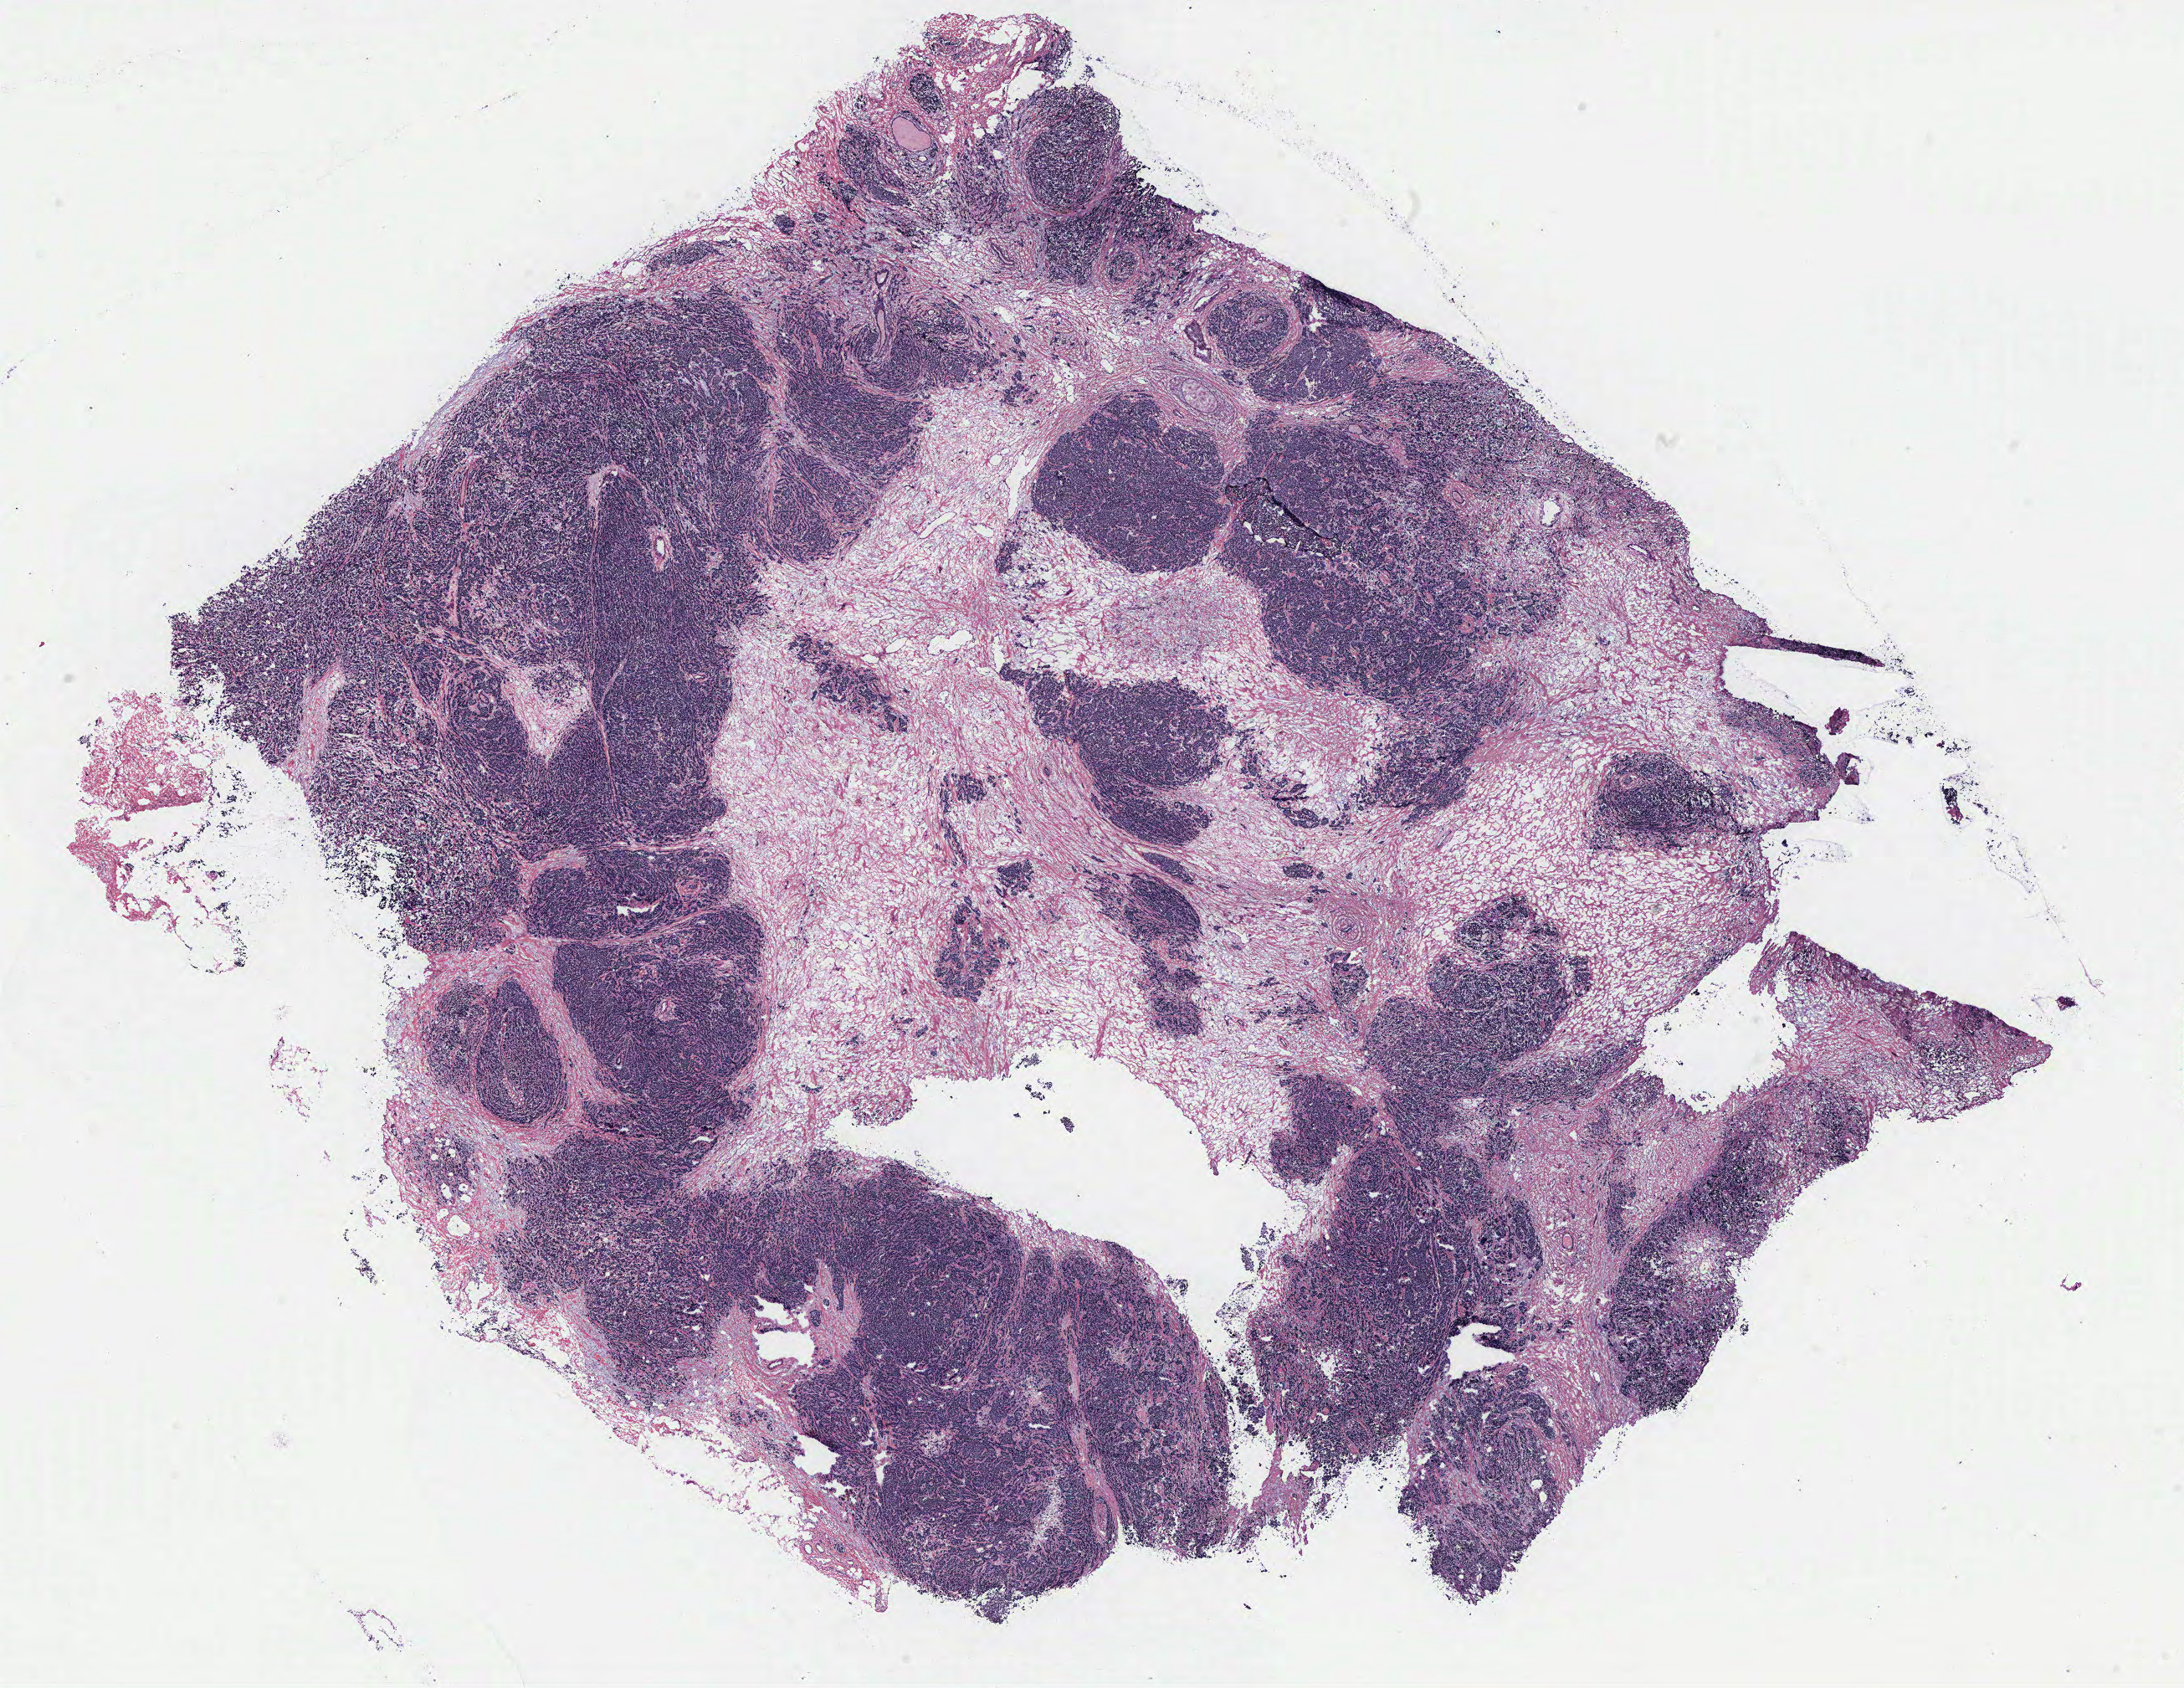
Whole-slide histology image, H&E, whole scanned area (about 20.9 x 16.1 mm, acquisition: 40x scan) shown as a low-resolution overview; breast, tissue type not recorded. 59-year-old female patient.
Patient diagnosis: Infiltrating duct carcinoma, NOS.